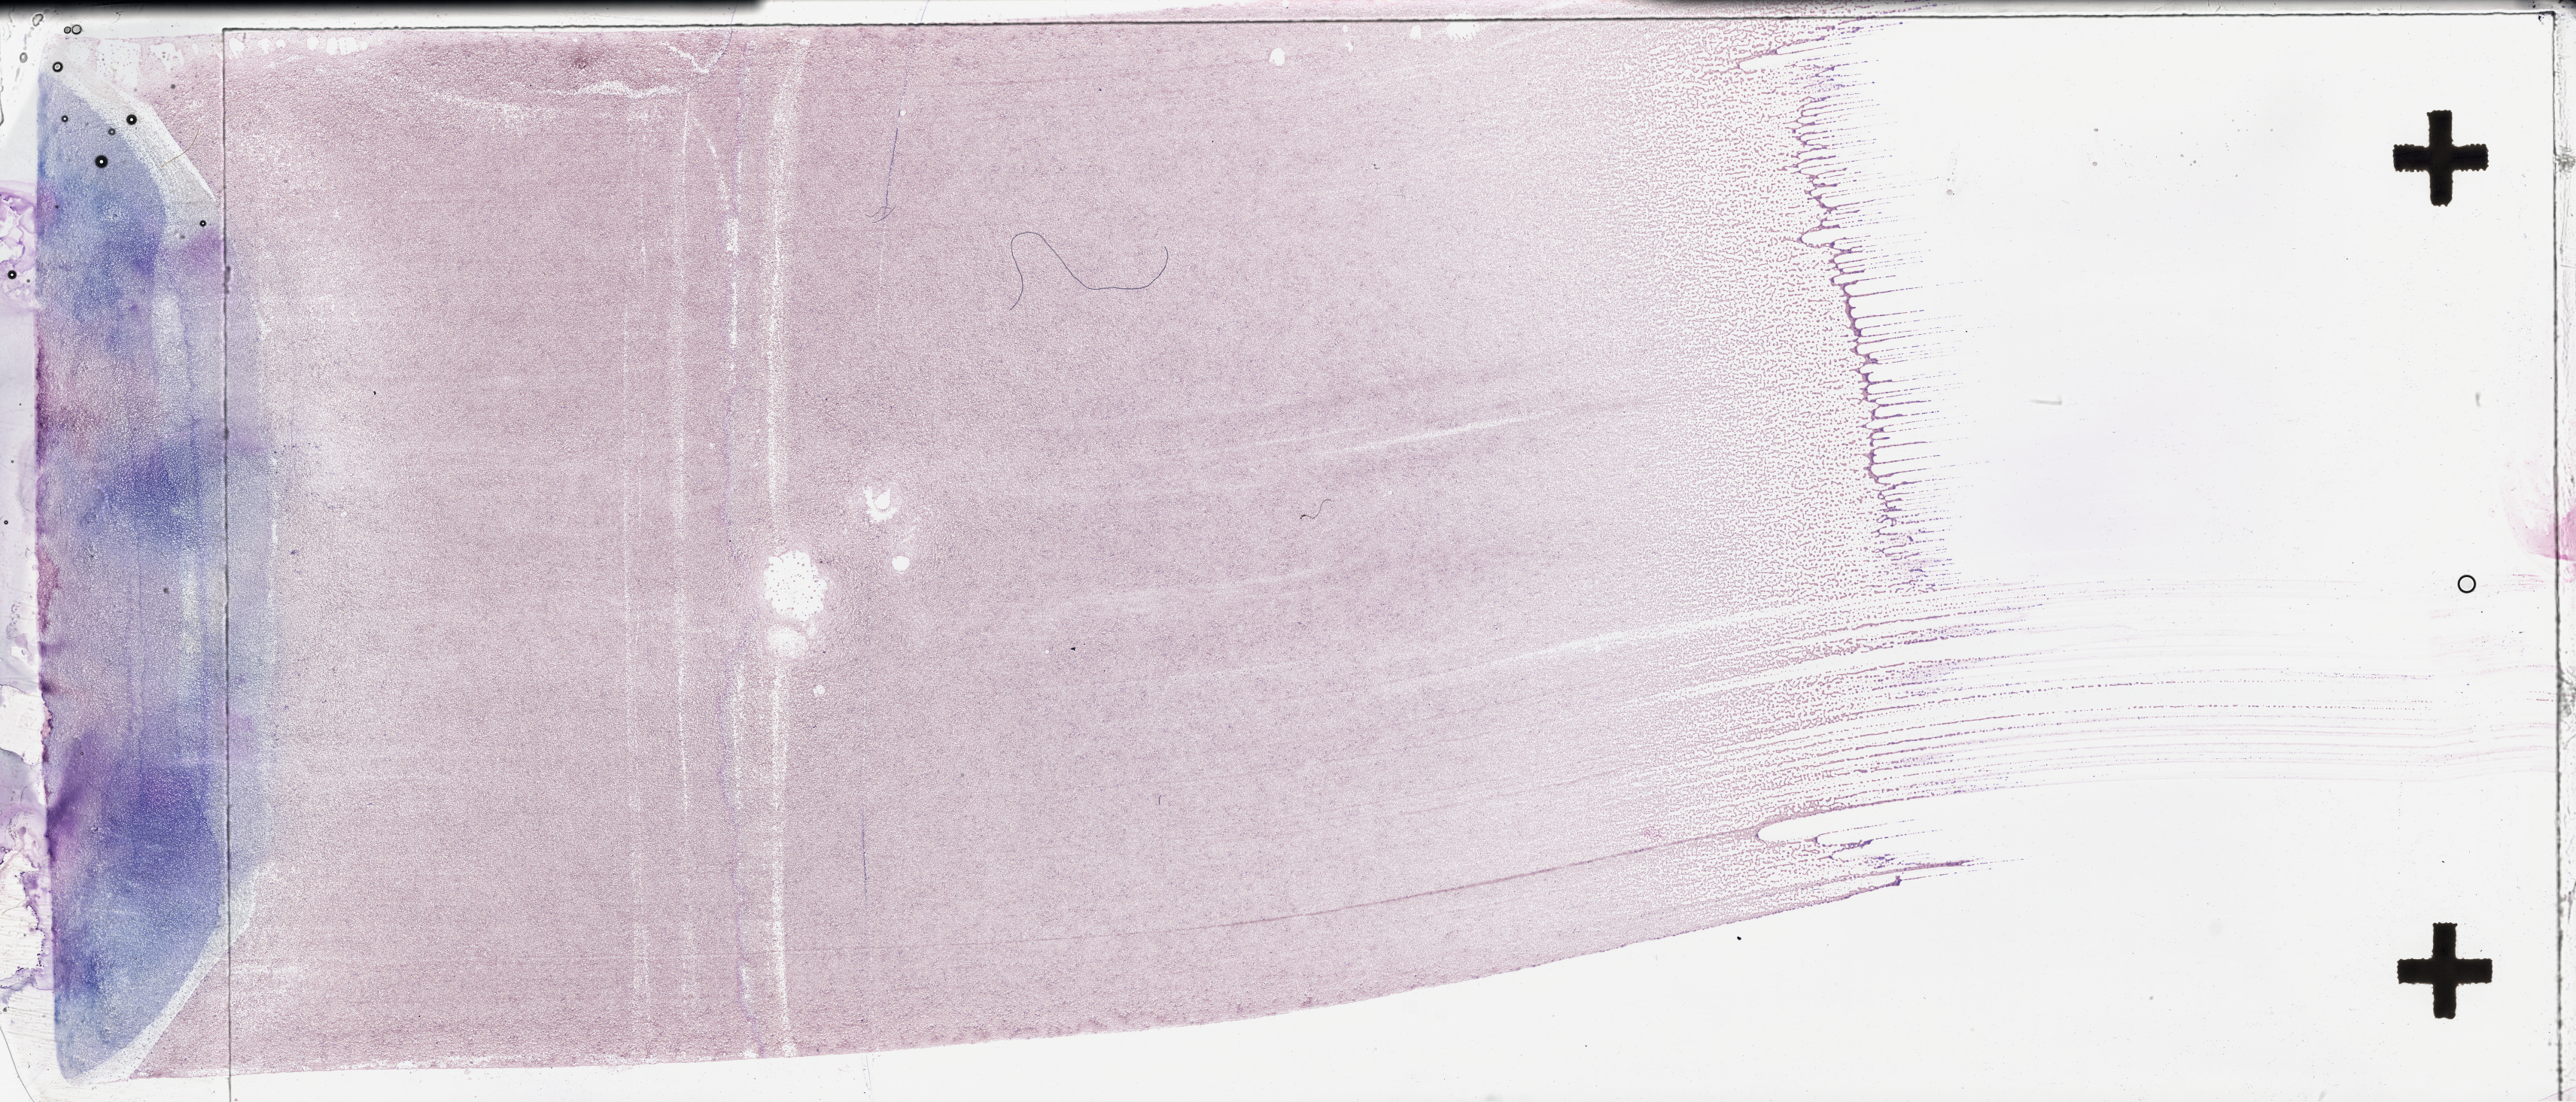
H&E whole-slide image — a low-resolution overview of the entire scanned area, about 55.3 x 23.7 mm; peripheral blood (leukaemic) sample. Male, 66 y/o.
FAB classification: M3. Diagnosis: Acute Myeloid Leukemia. WHO classification: Acute Promyelocytic Leukemia with t(15;17)(q22;q12); PML-RARA.